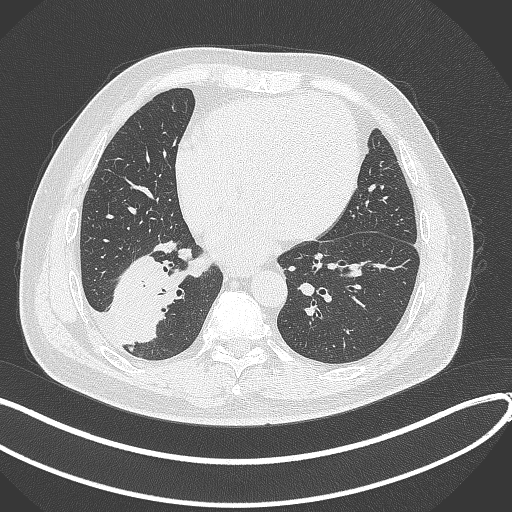
Chest CT, one axial slice; slice 130 of 360 in the series (ordered by position); reconstruction kernel B70f; 120 kVp; lung window (W 1500 / L -600 HU); 512 × 512 image matrix. Male patient, age 59 years.
Annotated regions visible in this slice (rectangle marked by the reading radiologist):
- lung tumour (recorded histology: adenocarcinoma): bounding box [x1, y1, x2, y2] px = [107, 243, 171, 343]